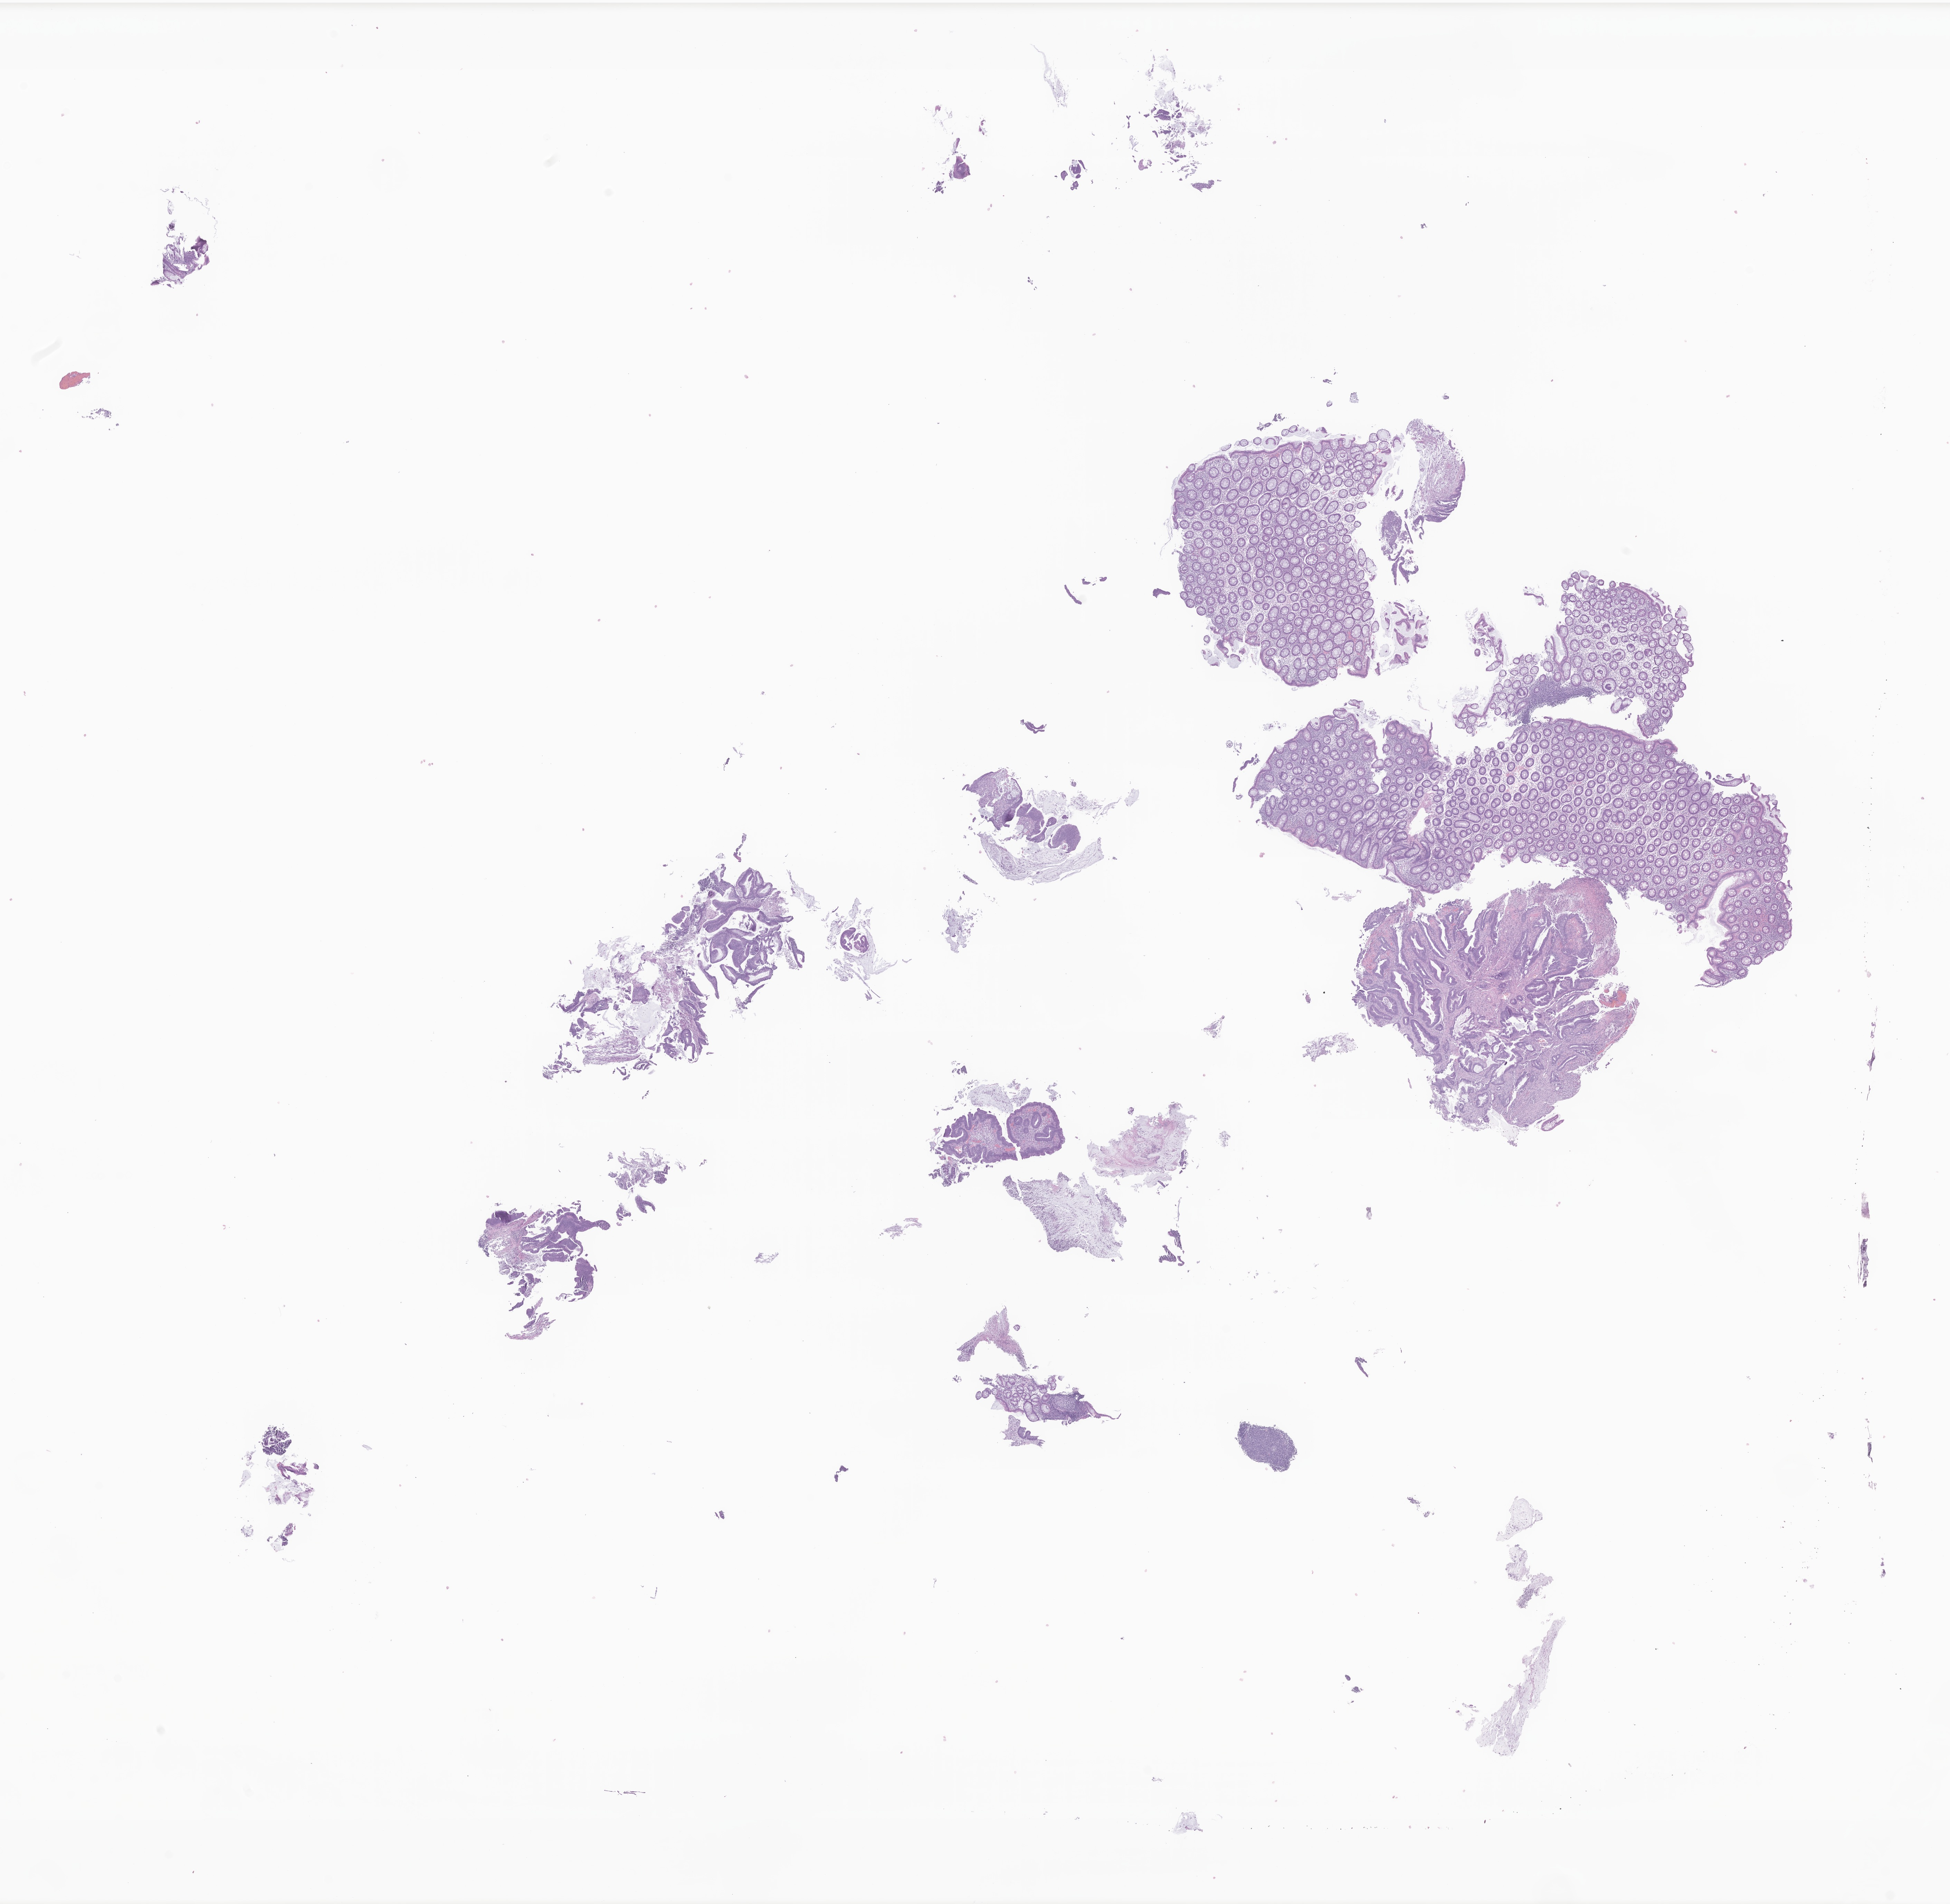
Whole-slide image, hematoxylin and eosin (H&E) stain of tumor tissue from the ascending colon, whole scanned area (about 23.8 x 23.2 mm) shown as a low-resolution overview, formalin-fixed paraffin-embedded section. Patient female; age 131 months (10 years 11 months).
Diagnosis (ICD-O-3 morphology term): Adenocarcinoma in situ in tubulovillous adenoma.